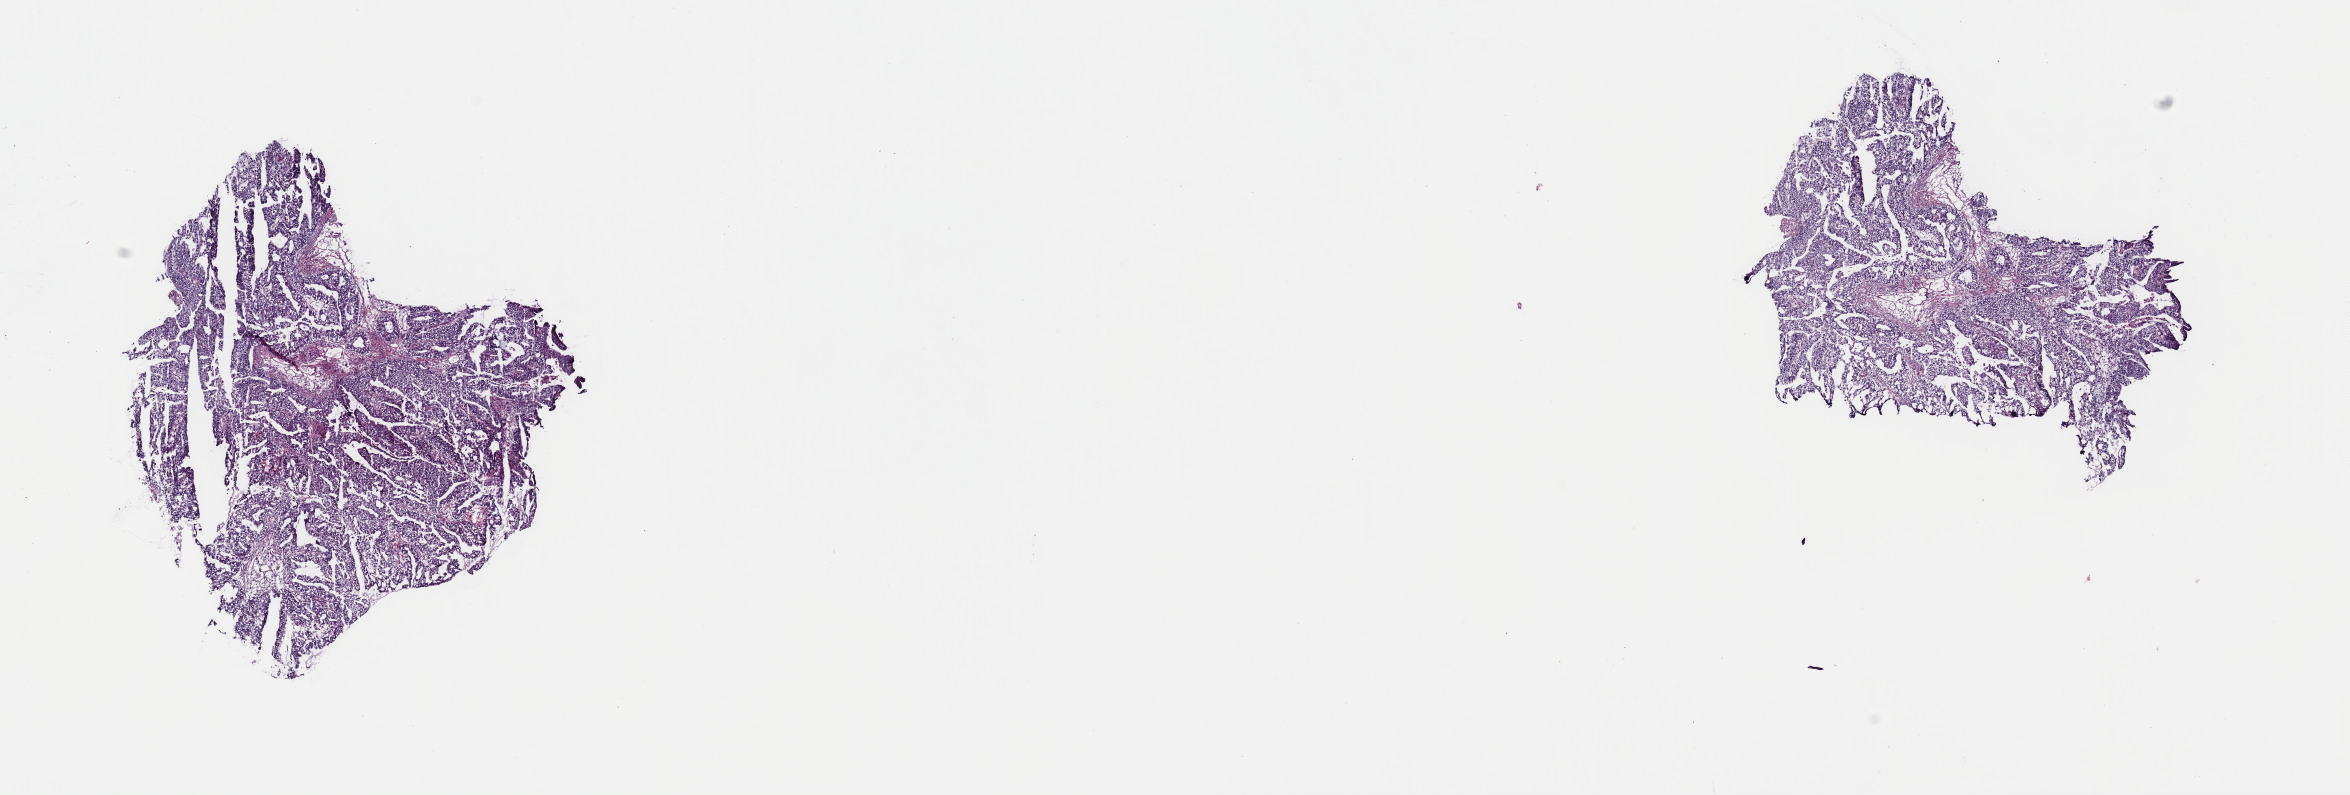
Whole-slide histology image, H&E — low-resolution overview of the scanned area, about 18.6 x 6.3 mm (from a 40x scan), frozen section from the top of the tissue portion, lung, primary tumour sample. Patient: female, age at initial diagnosis 61 years. Composition of this section per pathologist review: tumour cells 80%, tumour nuclei 90%, normal cells 0%, stromal cells 19%, necrosis 1%. Inflammatory infiltration, as recorded: lymphocyte infiltration 1%, monocyte infiltration 0%, neutrophil infiltration 0%.
AJCC pathologic stage: IB (7th edition). Histologic diagnosis: Adenocarcinoma, NOS (lower lobe, lung). TNM: T2a N0 MX. Laterality: right.